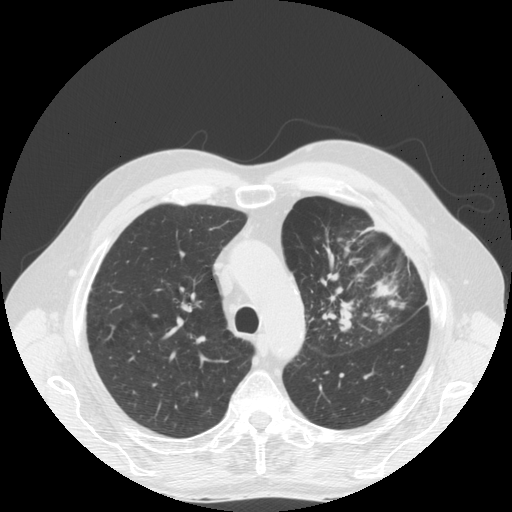
Low-dose screening chest CT, one axial slice. Slice 128 of 170 in the series (ordered by position). Reconstruction kernel STANDARD. 140 kVp. Lung window (W 1500 / L -600 HU). 512 × 512 image matrix, field of view 380 × 380 mm.
Annotated regions visible in this slice (expert manual segmentation):
- lesion 1 (tumor, upper lobe of left lung): bounding box (x1, y1, x2, y2) in pixels: (339, 301, 354, 332)